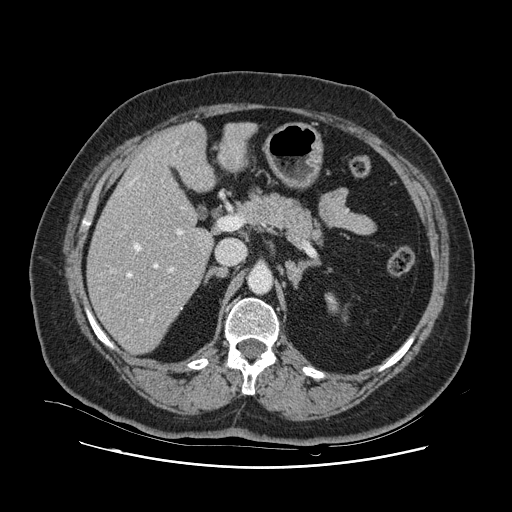
Contrast-enhanced abdominal CT, one axial slice; position 59 of 132 along the scan axis; 120 kVp; intravenous contrast given; soft-tissue window (W 400 / L 40 HU); 512 × 512 image matrix, field of view 391 × 391 mm. Female patient, age 73 years. Case-level facts recorded for this patient, not image findings: diagnosis: colorectal cancer liver metastases, imaged before liver resection; multiple liver metastases: no; largest metastasis: 7 cm; disease in both lobes: no.
Structures marked on this image (manually delineated by an expert):
- hepatic veins: bounding box <113,155,184,321> (left, top, right, bottom; pixels)
- liver: <89,124,252,354>
- planned liver remnant (the part of the liver to remain after resection): <89,149,213,354>
- portal vein (with intrahepatic branches): <169,230,187,272>